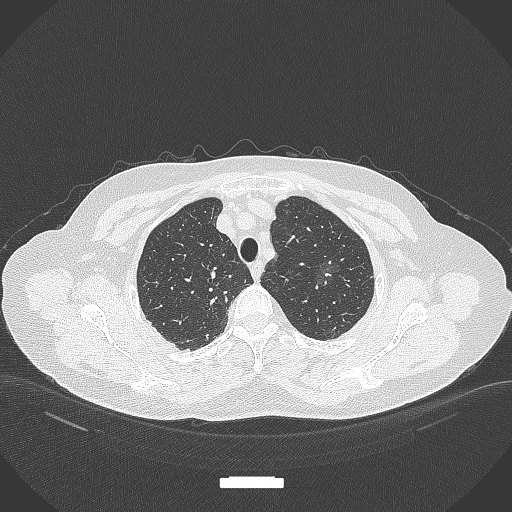
Chest CT, one axial slice. Reconstruction kernel B70f. Lung window (W 1500 / L -600 HU). 1 mm slice thickness. 512 × 512 image matrix. Female patient, age 64 years. From the clinical record (not read from this slice): clinical TNM (as recorded): T1c N0 M0; histopathological grade: G1.
Annotated regions visible in this slice (rectangle marked by the reading radiologist):
- lung tumour (recorded histology: adenocarcinoma): box from (x=312, y=257) to (x=344, y=293) px